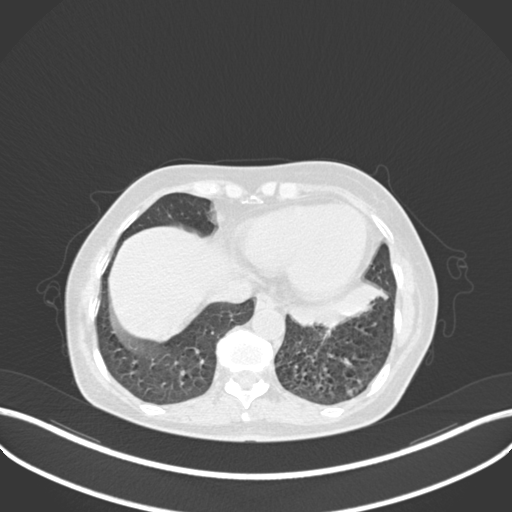
Chest CT, one axial slice. Position 65 of 270 along the scan axis. Reconstruction kernel B30f. 120 kVp. Lung window (W 1500 / L -600 HU). 1 mm slice thickness. 512 × 512 image matrix, field of view 400 × 400 mm. Patient: female, 63 years. Case-level facts recorded for this patient, not image findings: clinical TNM (as recorded): T1b N0 M0.
Annotated regions visible in this slice (bounding box drawn by a radiologist):
- lung tumour (recorded histology: adenocarcinoma): bounding box [x1, y1, x2, y2] px = [289, 281, 388, 328]